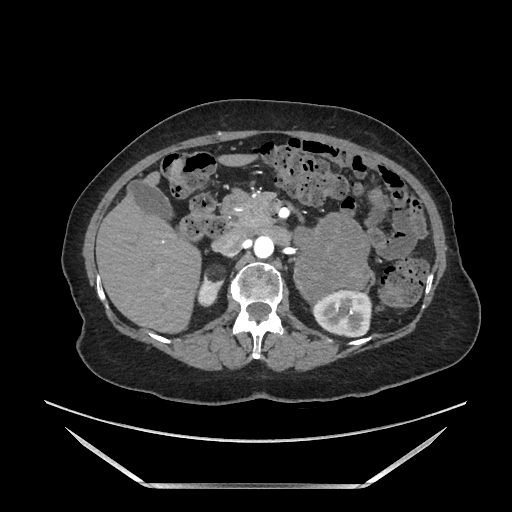
Contrast-enhanced abdominal CT, one axial slice; position 96 of 205 along the scan axis; soft-tissue window (W 400 / L 40 HU); 1.25 mm slice thickness; 512 × 512 image matrix, field of view 440 × 440 mm. Female patient. Case-level facts recorded for this patient, not image findings: diagnosis: adrenocortical carcinoma; tumour side: left adrenal; tumour size at pathology: 12.5 cm; Ki-67 index: 39 %.
Structures marked on this image (semi-automatic segmentation, software-assisted and operator-edited):
- mass: bounding box (x1, y1, x2, y2) in pixels: (297, 217, 369, 296)